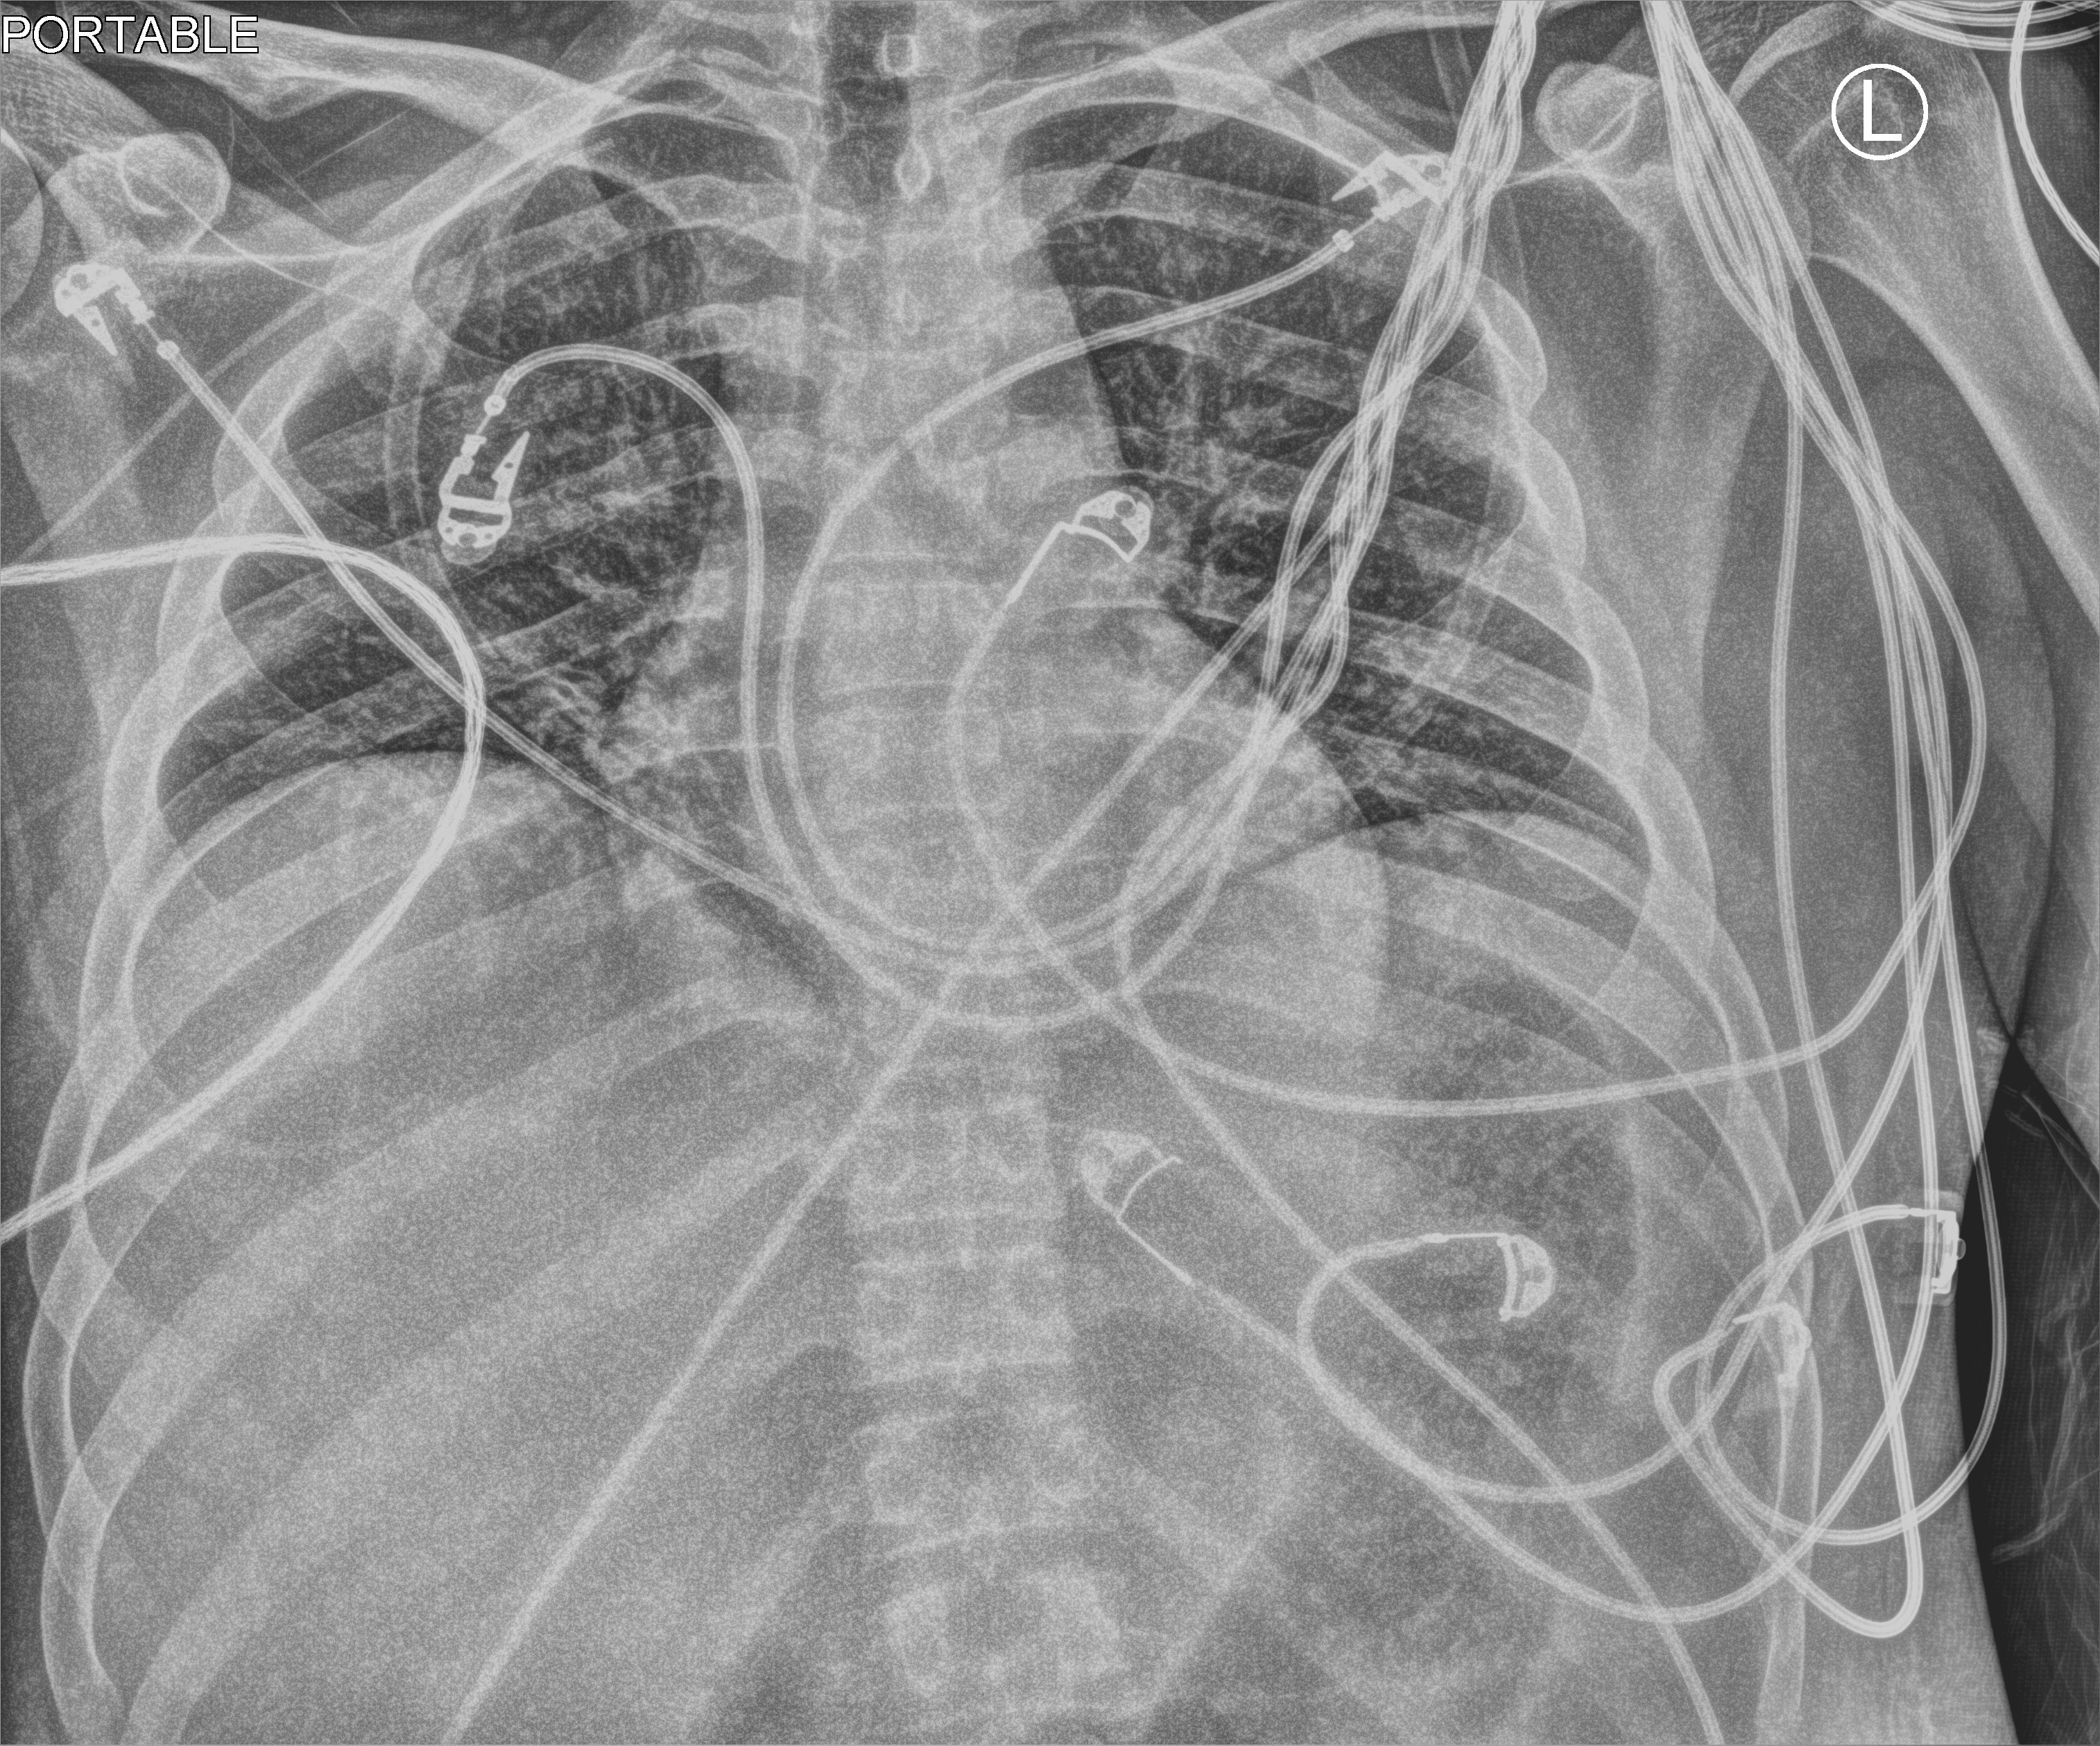
Portable chest radiograph; anteroposterior (AP) projection. Male patient hospitalised with COVID-19, age 18–59 years.
Admission-level facts for this patient (not findings on this image; timing relative to this image not recorded): other chronic lung disease (admission record): no.